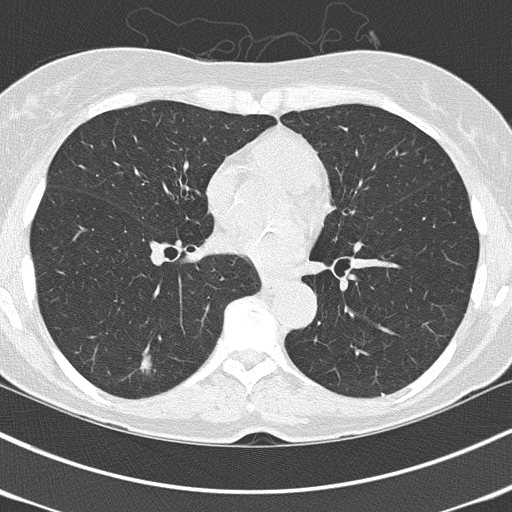
Low-dose screening chest CT, axial slice. Third screening round (two years after baseline). Lung window (W 1500 / L -600 HU). 2 mm slice thickness. Female participant, aged 67 years at enrolment. Current smoker at enrolment.
• Expert reader's lesion annotation, bounding box (x1, y1, x2, y2) in pixels: (127, 348, 167, 385).
• The screening reader recorded 3 non-calcified nodules or masses ≥4 mm on this exam (right lower lobe, right lower lobe, left lower lobe); which of them this box marks is not recorded.
• Lung cancer was diagnosed 64 days after this screen: adenocarcinoma, NOS, left lower lobe, poorly differentiated (G3), stage IA (AJCC 6th edition), 25 mm at pathology.